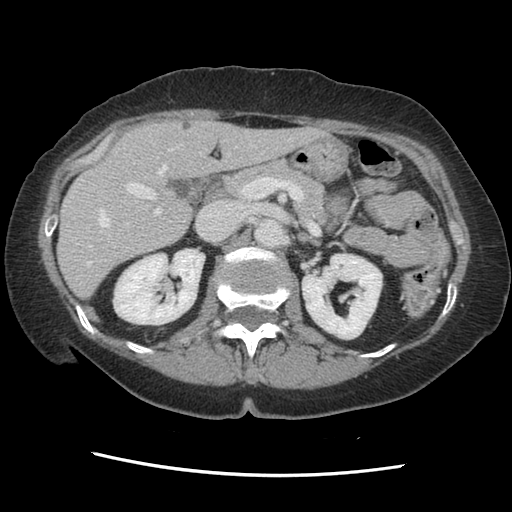
Contrast-enhanced abdominal CT, one axial slice; soft-tissue window (W 400 / L 40 HU); 2.5 mm slice thickness; 512 × 512 image matrix. Female patient, age 61 years. Case-level facts recorded for this patient, not image findings: diagnosis: colorectal cancer liver metastases, imaged before liver resection; multiple liver metastases: no; largest metastasis: 2.4 cm; disease in both lobes: no.
Outlined on this slice (manually delineated by an expert):
- hepatic veins: bounding box <88,144,253,265> (left, top, right, bottom; pixels)
- liver: <58,121,316,297>
- planned liver remnant (the part of the liver to remain after resection): <58,122,316,297>
- portal vein (with intrahepatic branches): <89,162,161,247>
- liver metastasis: <182,121,192,131>